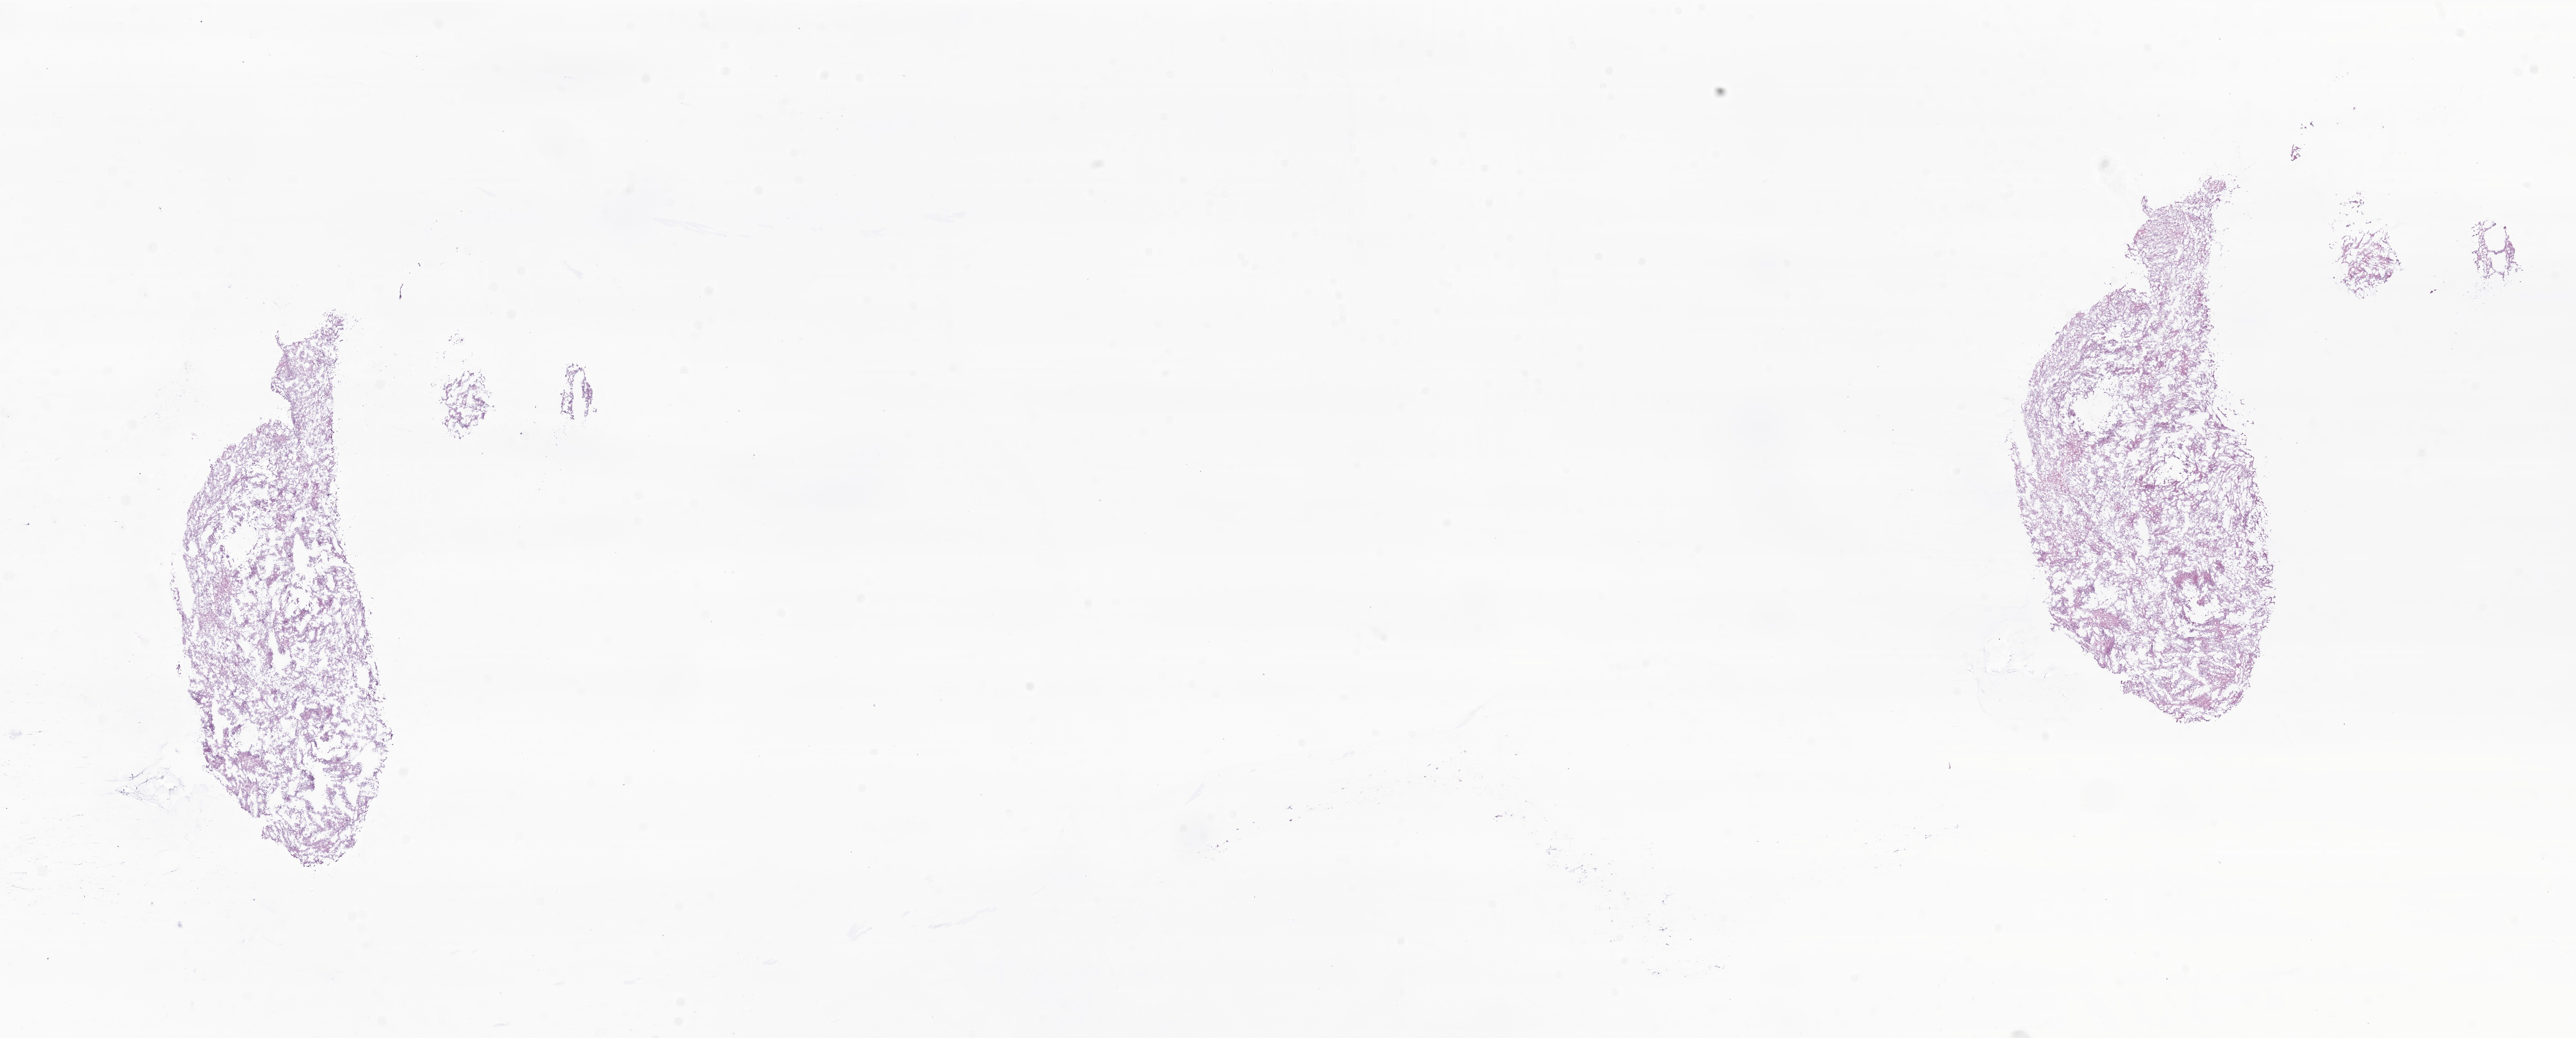
Digitized haematoxylin and eosin-stained section of tumor tissue from the brain — shown as a low-resolution overview of the whole scanned area (about 28.9 x 11.6 mm); frozen section. Patient female; age 137 months (11 years 5 months).
• diagnosis: Pilocytic astrocytoma